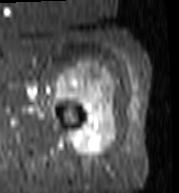
MRI of an extremity soft-tissue mass, one axial slice; position 86 of 103 along the scan axis; STIR; MR volume resampled by the dataset authors to the PET/CT grid (not the native acquisition matrix); 179 × 193 image matrix, field of view 175 × 188 mm. Female patient. Case-level facts recorded for this patient, not image findings: histological type: undifferentiated – high grade; grade: high; site of the primary tumour: left thigh.
Outlined on this slice (expert contour drawn on MRI and transferred to this co-registered scan by the dataset authors):
- gross tumour volume including surrounding oedema: bounding box [x1, y1, x2, y2] px = [54, 62, 117, 163]
- gross tumour volume (mass): [56, 64, 117, 161]